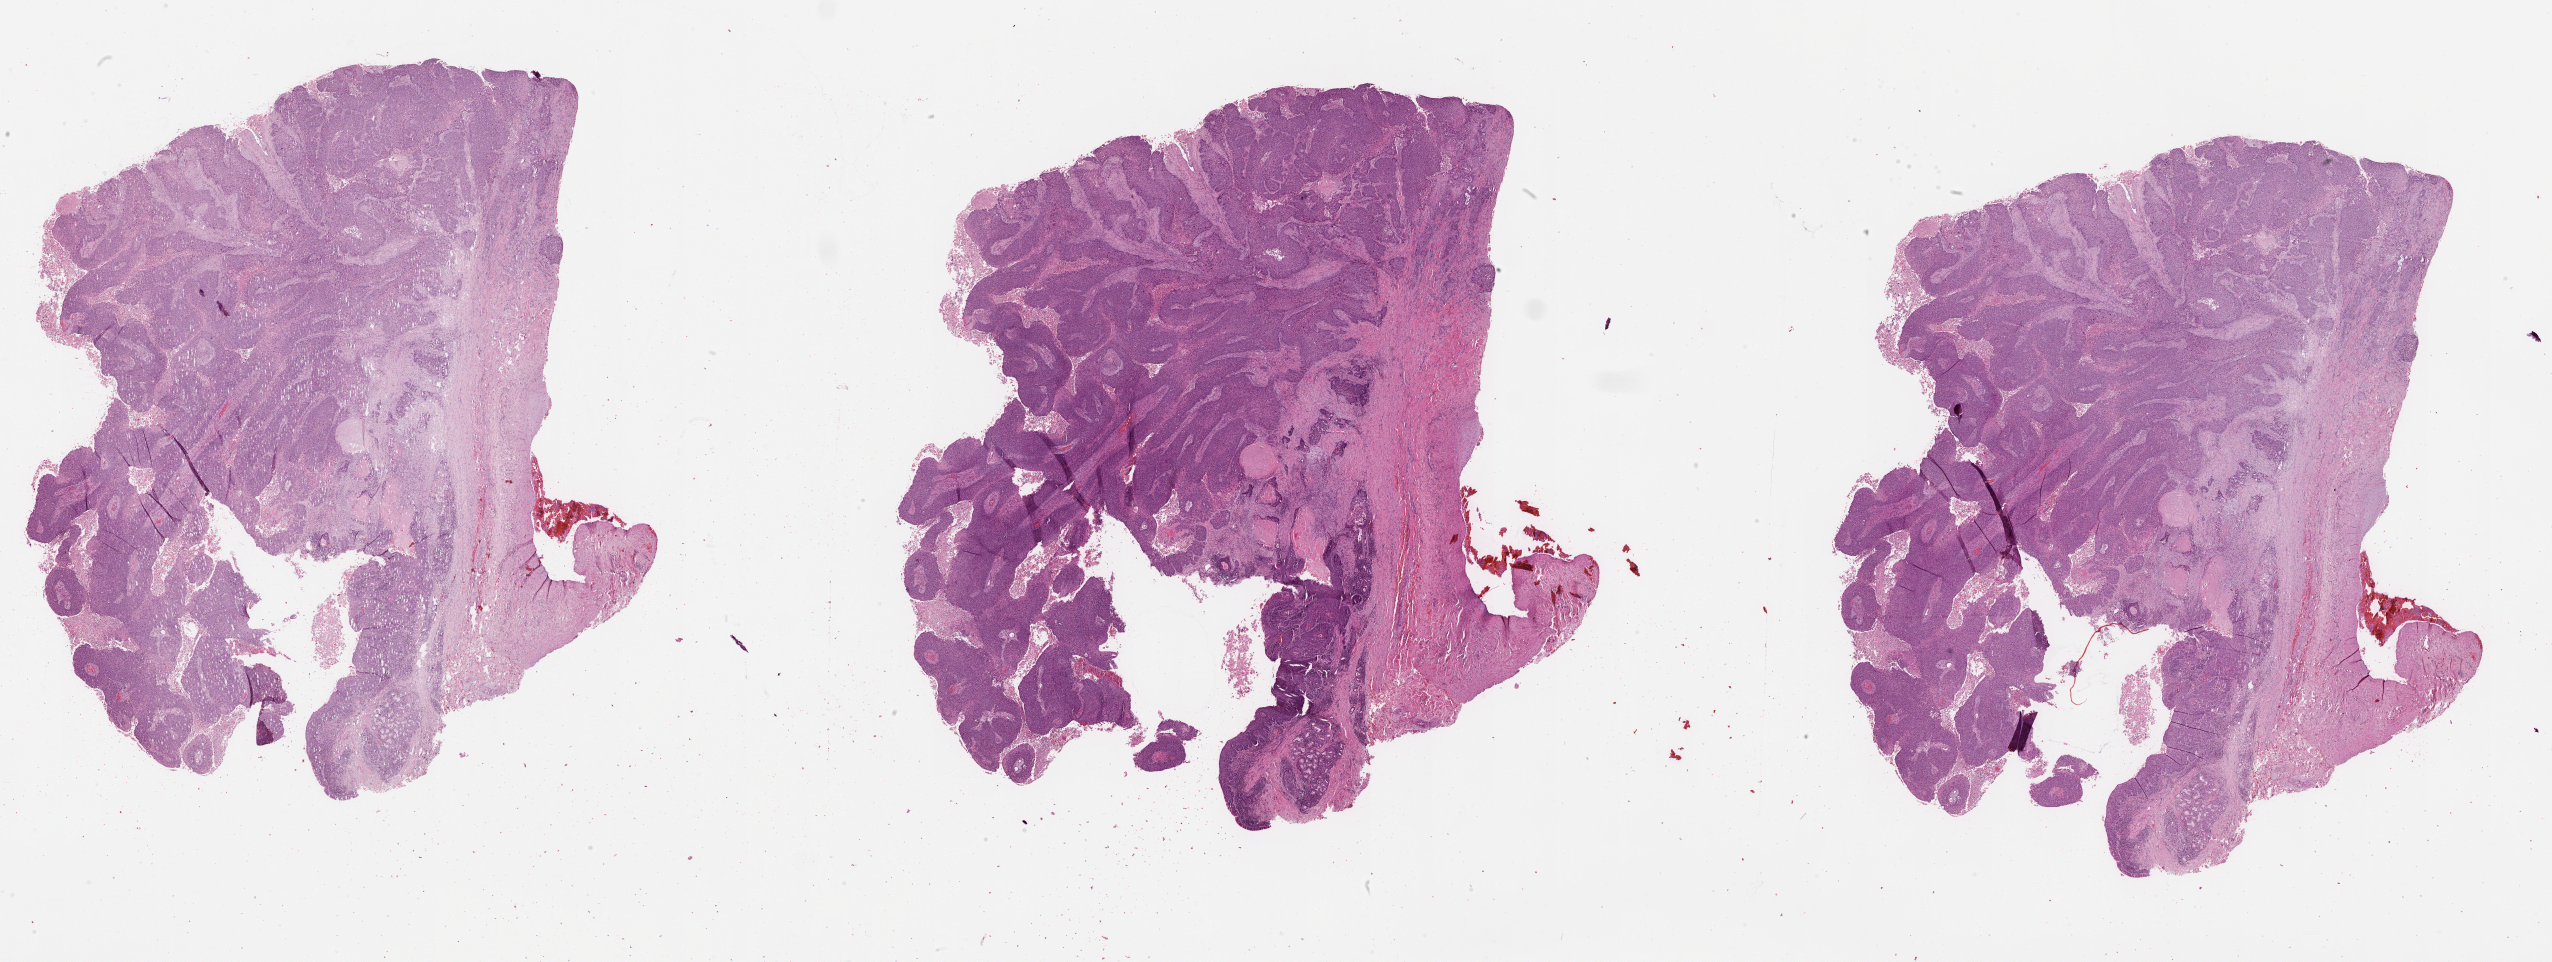
Digitized H&E tissue section (whole slide) — shown as a low-resolution overview of the whole scanned area (about 41.1 x 15.5 mm, slide scanned at 20x); tumour tissue sample, lung. 43-year-old male patient.
Patient diagnosis (cohort enrolment): squamous cell carcinoma (lung).